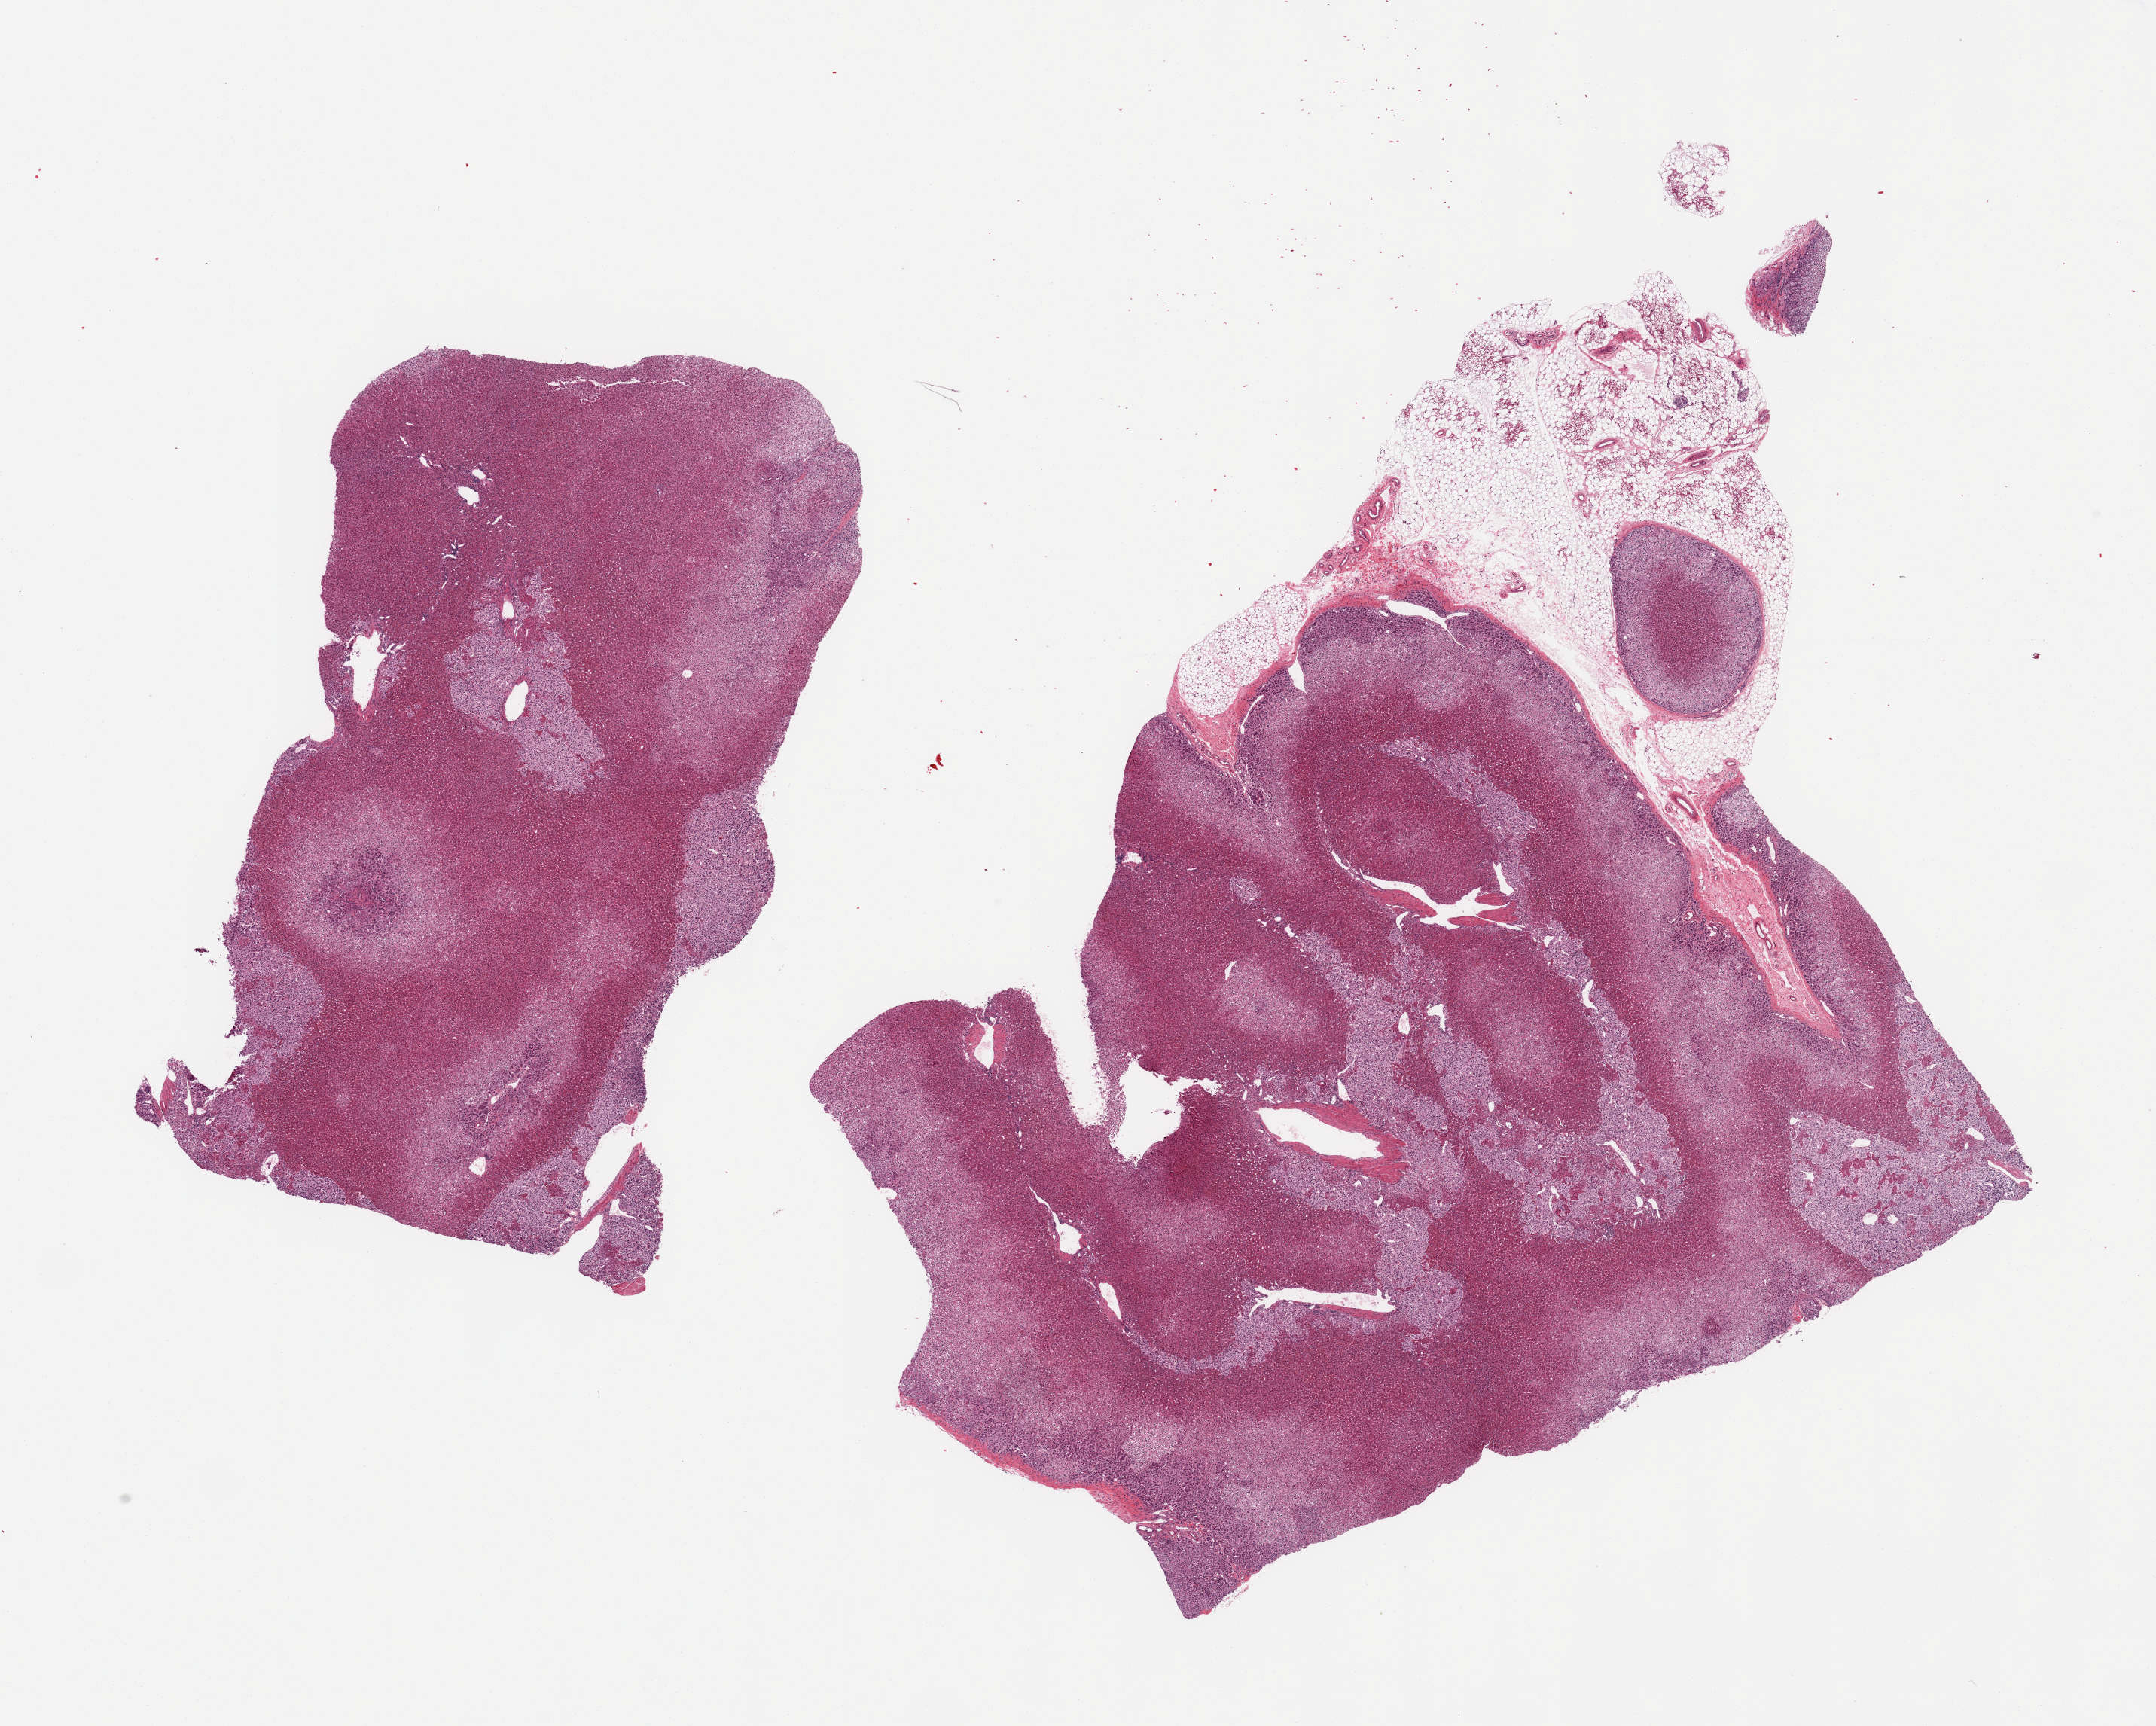
Whole-slide image, H&E stain — a low-resolution overview of the entire scanned area, about 22.6 x 18.1 mm, PAXgene-fixed paraffin-embedded (PFPE) section, sampled site (target tissue): adrenal gland, donor tissue sample. Female donor.
Pathologist's review note for this sample: 2 pieces; adrenal cortex; up to 4mm (20%) external fat attached to one sample.